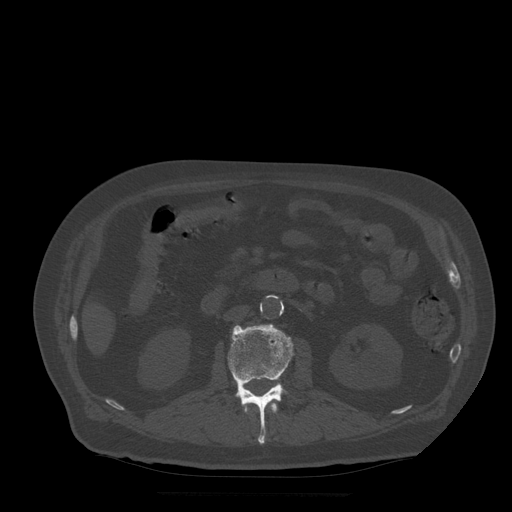
CT including the spine, one axial slice. Slice 167 of 522 in the series (ordered by position). Bone window (W 1800 / L 400 HU). 512 × 512 image matrix, field of view 420 × 420 mm. Patient age 72 years. Case-level facts recorded for this patient, not image findings: primary cancer: prostate.
Structures marked on this image (semi-automatic segmentation, software-assisted and operator-edited):
- L1 vertebra: bounding box [x1, y1, x2, y2] px = [245, 403, 278, 414]
- L2 vertebra: [228, 324, 293, 444]